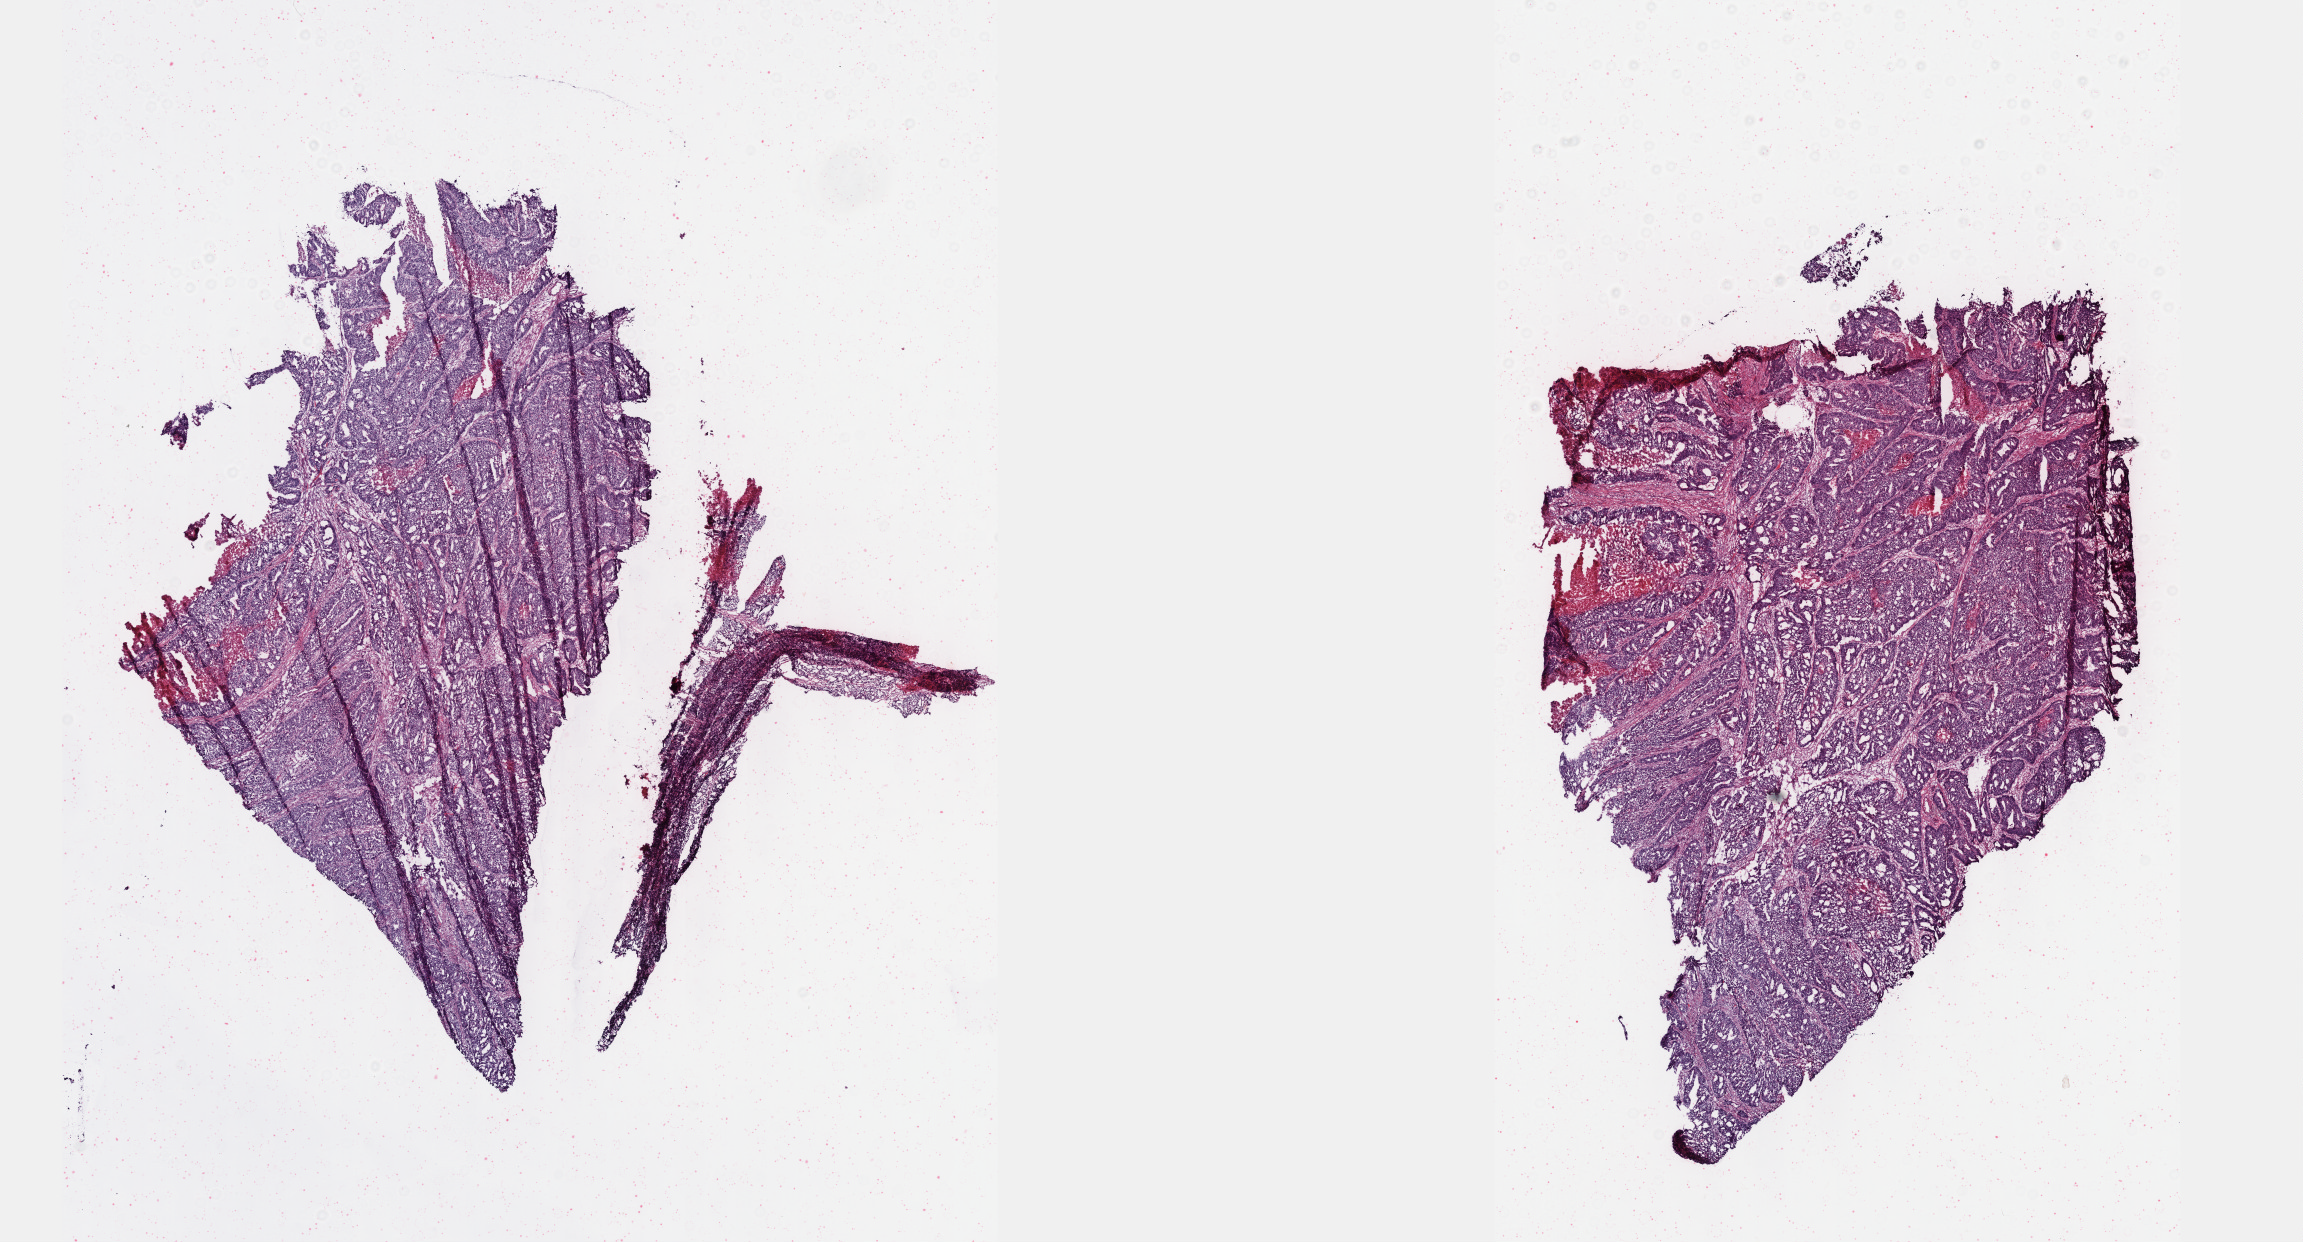
Digitized H&E tissue section (whole slide), shown as a low-resolution overview of the whole scanned area (about 18.6 x 10.0 mm, slide scanned at 40x), frozen section, colon, primary tumour sample. Female patient; age at initial diagnosis 68 years. Composition of this section per pathologist review: tumour cells 90%, tumour nuclei 95%, normal cells 0%, stromal cells 5%, necrosis 5%. Infiltration values recorded for this section: lymphocyte infiltration 1%, monocyte infiltration 1%, neutrophil infiltration 1%.
TNM: T3 N1 M1. AJCC pathologic stage: IV (6th edition). Diagnosis: Carcinoma, NOS. Lymph nodes positive (case pathology): 1 of 12 examined.